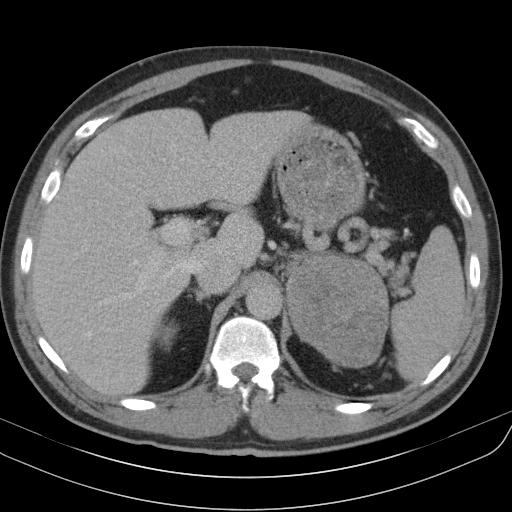
Contrast-enhanced abdominal CT, one axial slice. Slice 73 of 91 in the series (ordered by position). 130 kVp. Intravenous contrast given. Soft-tissue window (W 400 / L 40 HU). 5 mm slice thickness. 512 × 512 image matrix, field of view 370 × 370 mm. Male patient, age 51 years. Case-level facts recorded for this patient, not image findings: diagnosis: adrenocortical carcinoma; tumour side: left adrenal; tumour size at pathology: 18 cm; Ki-67 index: 40 %; stage (as recorded): 3.
Annotated regions visible in this slice (semi-automatic segmentation, software-assisted and operator-edited):
- mass: box from (x=288, y=257) to (x=388, y=365) px